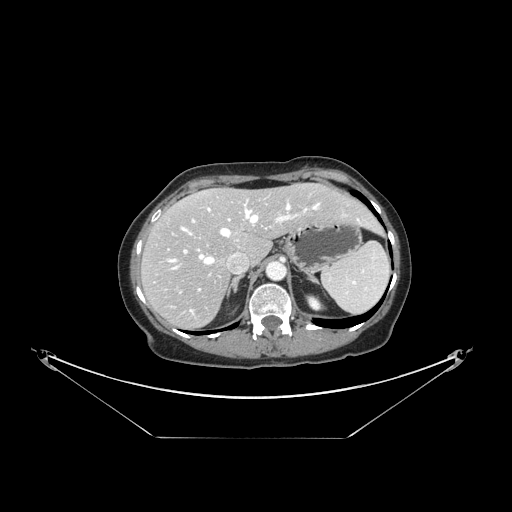
Contrast-enhanced abdominal CT, one axial slice. Slice 108 of 148 in the series (ordered by position). 120 kVp. Intravenous contrast given. Soft-tissue window (W 400 / L 40 HU). 2.5 mm slice thickness. 512 × 512 image matrix, field of view 500 × 500 mm. Female patient, age 73 years. Case-level facts recorded for this patient, not image findings: diagnosis: colorectal cancer liver metastases, imaged before liver resection; multiple liver metastases: no; largest metastasis: 1 cm; disease in both lobes: no.
Annotated regions visible in this slice (expert manual segmentation):
- hepatic veins: bounding box (x1, y1, x2, y2) in pixels: (170, 202, 360, 311)
- liver: (143, 184, 378, 328)
- planned liver remnant (the part of the liver to remain after resection): (168, 184, 377, 260)
- portal vein (with intrahepatic branches): (183, 204, 307, 291)